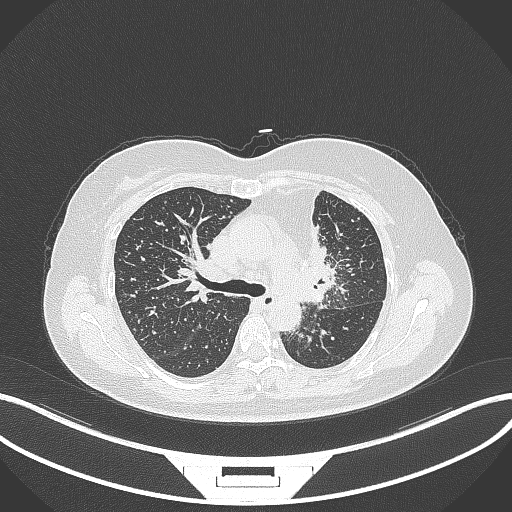
Chest CT, one axial slice. Reconstruction kernel B70f. Lung window (W 1500 / L -600 HU). 1 mm slice thickness. 512 × 512 image matrix, field of view 400 × 400 mm. Female patient, age 49 years. From the clinical record (not read from this slice): clinical TNM (as recorded): T1c N0 M1.
Structures marked on this image (rectangle marked by the reading radiologist):
- lung tumour (recorded histology: adenocarcinoma): bounding box <295,222,337,303> (left, top, right, bottom; pixels)